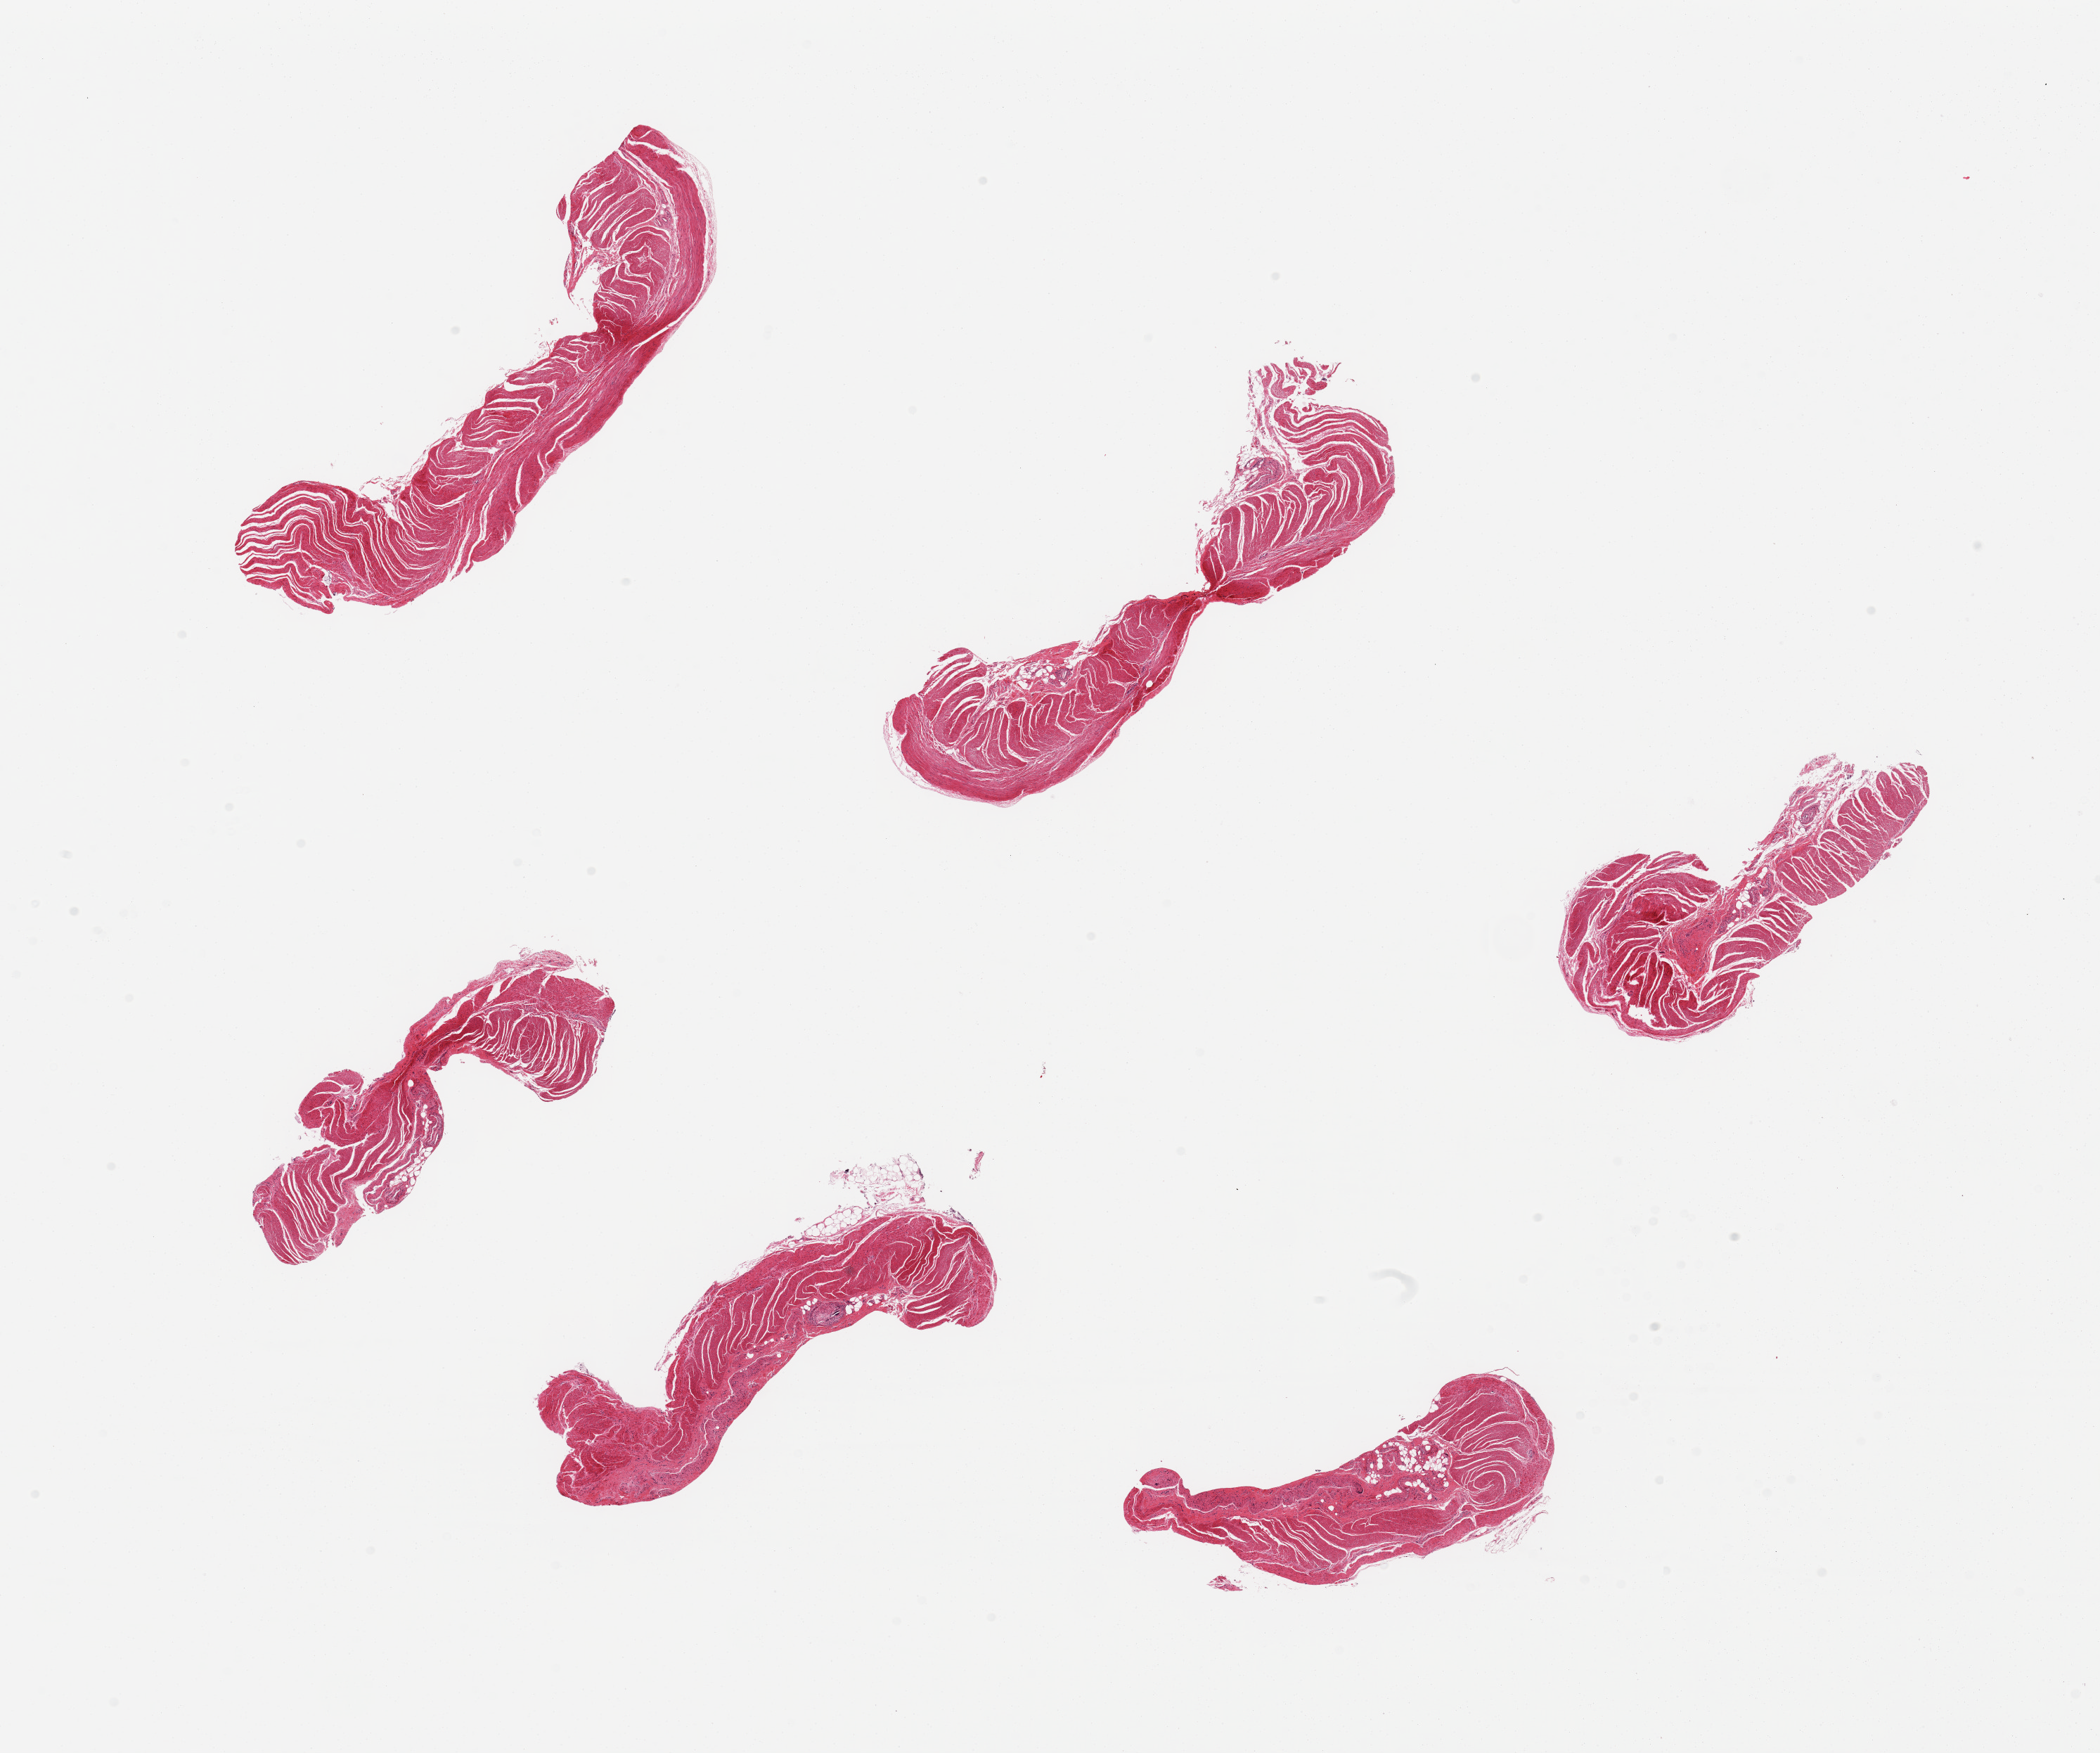
Haematoxylin and eosin whole-slide image, whole scanned area (about 23.6 x 19.7 mm, from a 20x scan) shown as a low-resolution overview. PAXgene-fixed, paraffin-embedded tissue. Section of sigmoid colon (target tissue). Tissue donor sample.
Reviewer comment on this tissue sample: 6 pieces, all muscularis, good specimens.